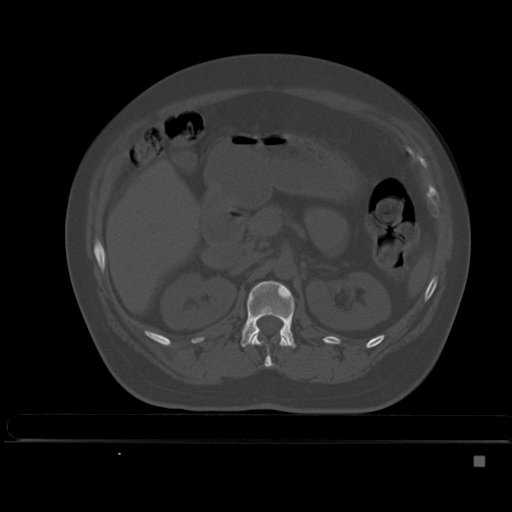
CT including the spine, one axial slice; position 201 of 495 along the scan axis; bone window (W 1800 / L 400 HU); 1.5 mm slice thickness; 512 × 512 image matrix, field of view 404 × 404 mm. Female patient, age 33 years. From the clinical record (not read from this slice): primary cancer: breast.
Structures marked on this image (semi-automatic segmentation, software-assisted and operator-edited):
- L1 vertebra: bounding box (x1, y1, x2, y2) in pixels: (240, 281, 296, 348)
- T12 vertebra: (249, 334, 290, 368)